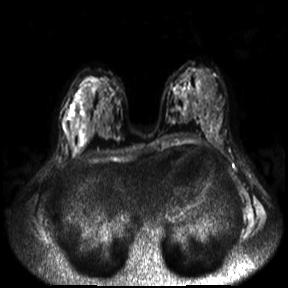
Breast MRI, one axial slice. Slice 16 of 30 in the series (ordered by position). Diffusion-weighted series; image 2 of 4 stored at this slice position (different b-values; order by instance number). 3 T. 288 × 288 image matrix, field of view 360 × 360 mm. Female patient.
Outlined on this slice (expert manual segmentation):
- tumour on diffusion-weighted imaging: box from (x=69, y=106) to (x=75, y=116) px